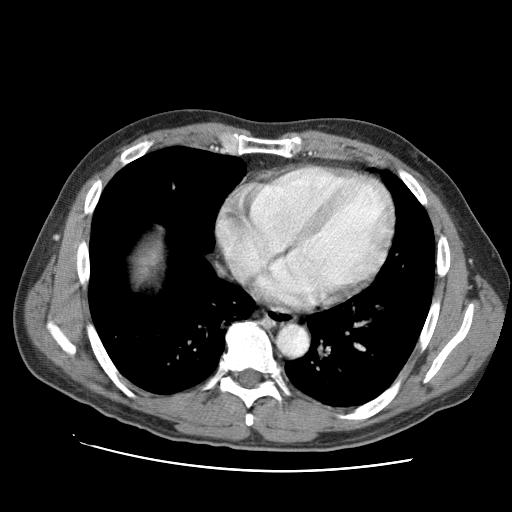
Contrast-enhanced abdominal CT (liver protocol), one axial slice; reconstruction kernel STANDARD; 120 kVp; one of 2 acquisitions stored at this slice position; soft-tissue window (W 400 / L 40 HU); 512 × 512 image matrix. Case-level facts recorded for this patient, not image findings: diagnosis: hepatocellular carcinoma (patient treated with transarterial chemoembolisation; whether this scan precedes or follows treatment is not stated here); TNM stage (as recorded): Stage-IVA; Child-Pugh class: A.
Structures marked on this image (semi-automatic segmentation, software-assisted and operator-edited):
- liver parenchyma outside the tumour (the mass and vessels are separate outlines, so this box may not span the whole liver): bounding box <138,244,162,276> (left, top, right, bottom; pixels)